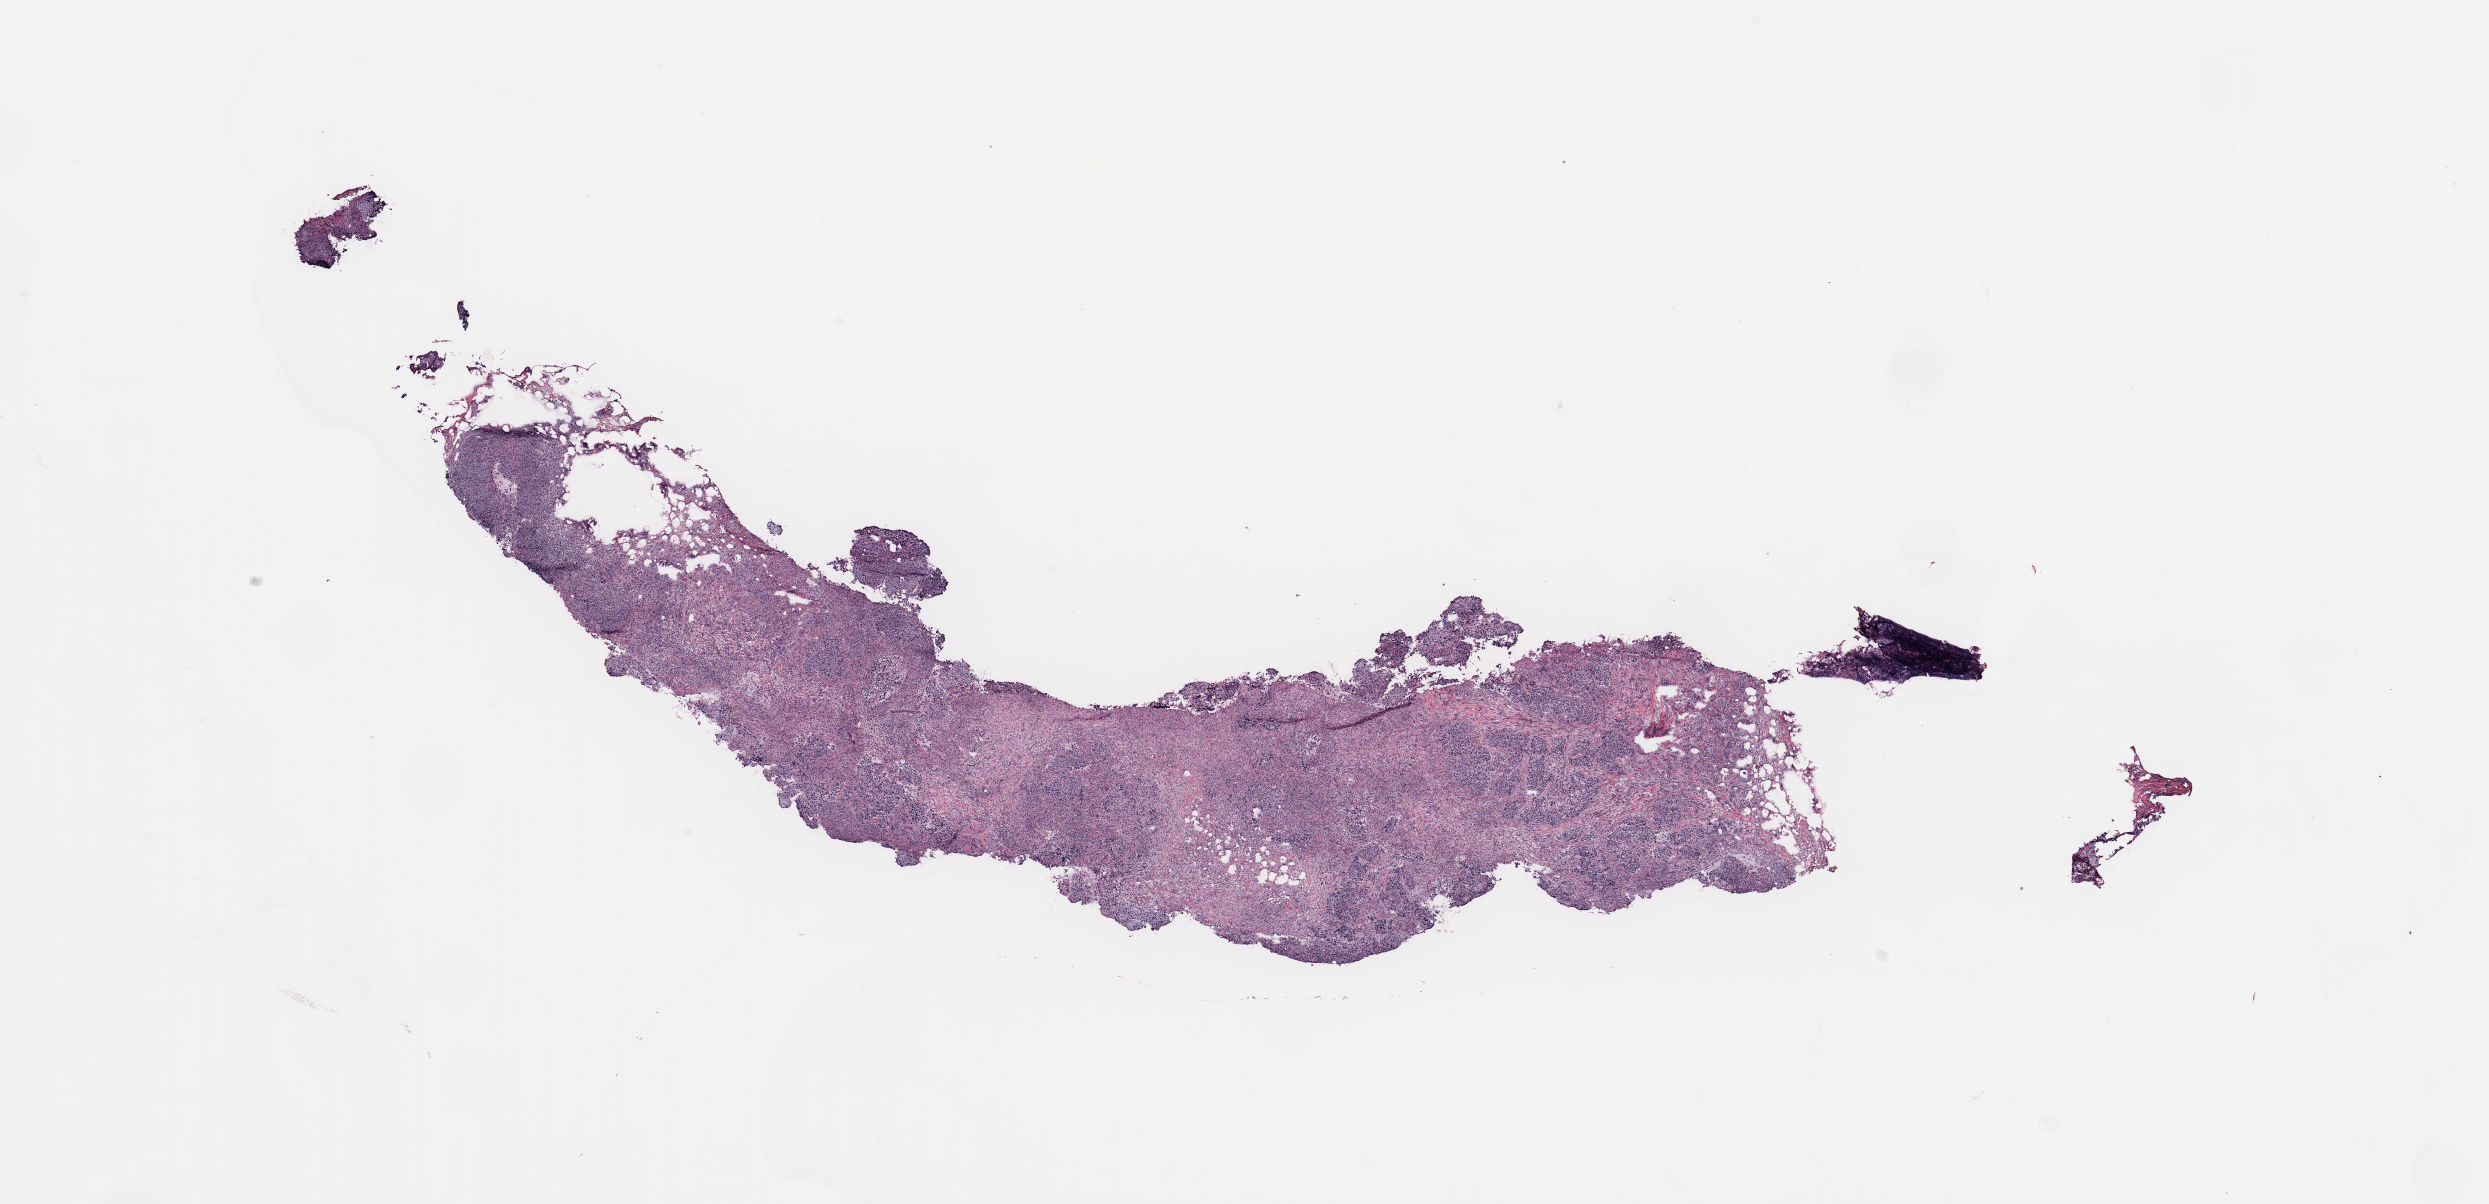
H&E whole-slide image — low-resolution overview of the scanned area, about 19.7 x 9.5 mm (slide scanned at 20x), breast, tissue type not recorded.
Patient diagnosis (cohort enrolment): breast cancer (breast).